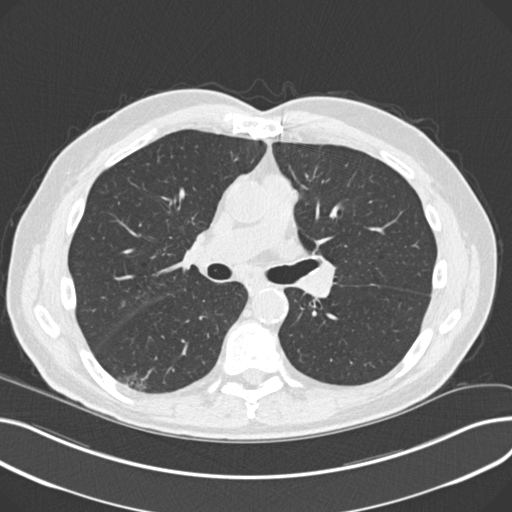
Low-dose screening chest CT, one axial slice. Slice 126 of 230 in the series (ordered by position). Reconstruction kernel B30f. 120 kVp. Lung window (W 1500 / L -600 HU). 2 mm slice thickness. 512 × 512 image matrix, field of view 372 × 372 mm.
Structures marked on this image (outlined manually by an expert reader):
- lesion 1 (nodule, lower lobe of right lung): bounding box [x1, y1, x2, y2] px = [124, 375, 148, 390]